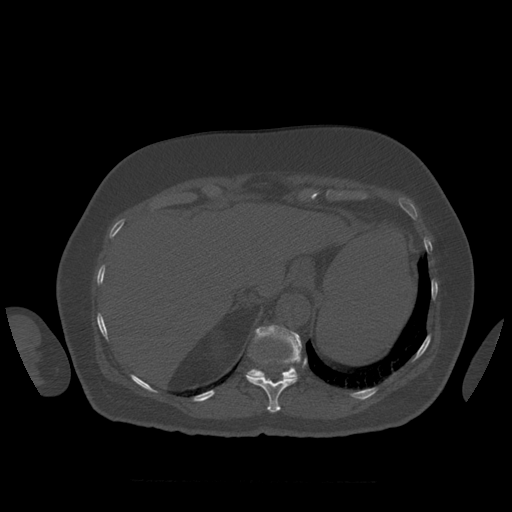
CT including the spine, one axial slice. Position 314 of 399 along the scan axis. Reconstruction kernel STANDARD. 120 kVp. Bone window (W 1800 / L 400 HU). 1.25 mm slice thickness. 512 × 512 image matrix, field of view 404 × 404 mm. Patient age 81 years. From the clinical record (not read from this slice): primary cancer: renal.
Structures marked on this image (semi-automatic segmentation, software-assisted and operator-edited):
- T11 vertebra: bounding box [x1, y1, x2, y2] px = [247, 360, 297, 413]
- T12 vertebra: [246, 325, 302, 380]